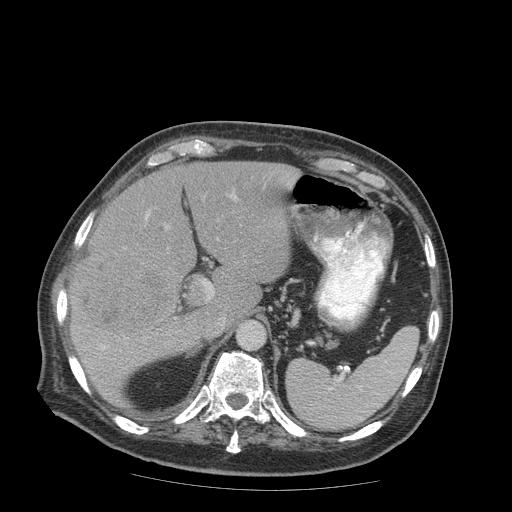
Contrast-enhanced abdominal CT (liver protocol), one axial slice; position 56 of 99 along the scan axis; reconstruction kernel STANDARD; soft-tissue window (W 400 / L 40 HU); 512 × 512 image matrix. From the clinical record (not read from this slice): diagnosis: hepatocellular carcinoma (patient treated with transarterial chemoembolisation; whether this scan precedes or follows treatment is not stated here); TNM stage (as recorded): Stage-IIIB; Child-Pugh class: A; tumour differentiation: well differentiated; tumour nodularity: multinodular.
Structures marked on this image (semi-automatically segmented with operator editing):
- liver parenchyma outside the tumour (the mass and vessels are separate outlines, so this box may not span the whole liver): box from (x=68, y=162) to (x=300, y=406) px
- mass: (x=73, y=248)–(x=179, y=338)
- liver vessels: (x=100, y=195)–(x=237, y=350)